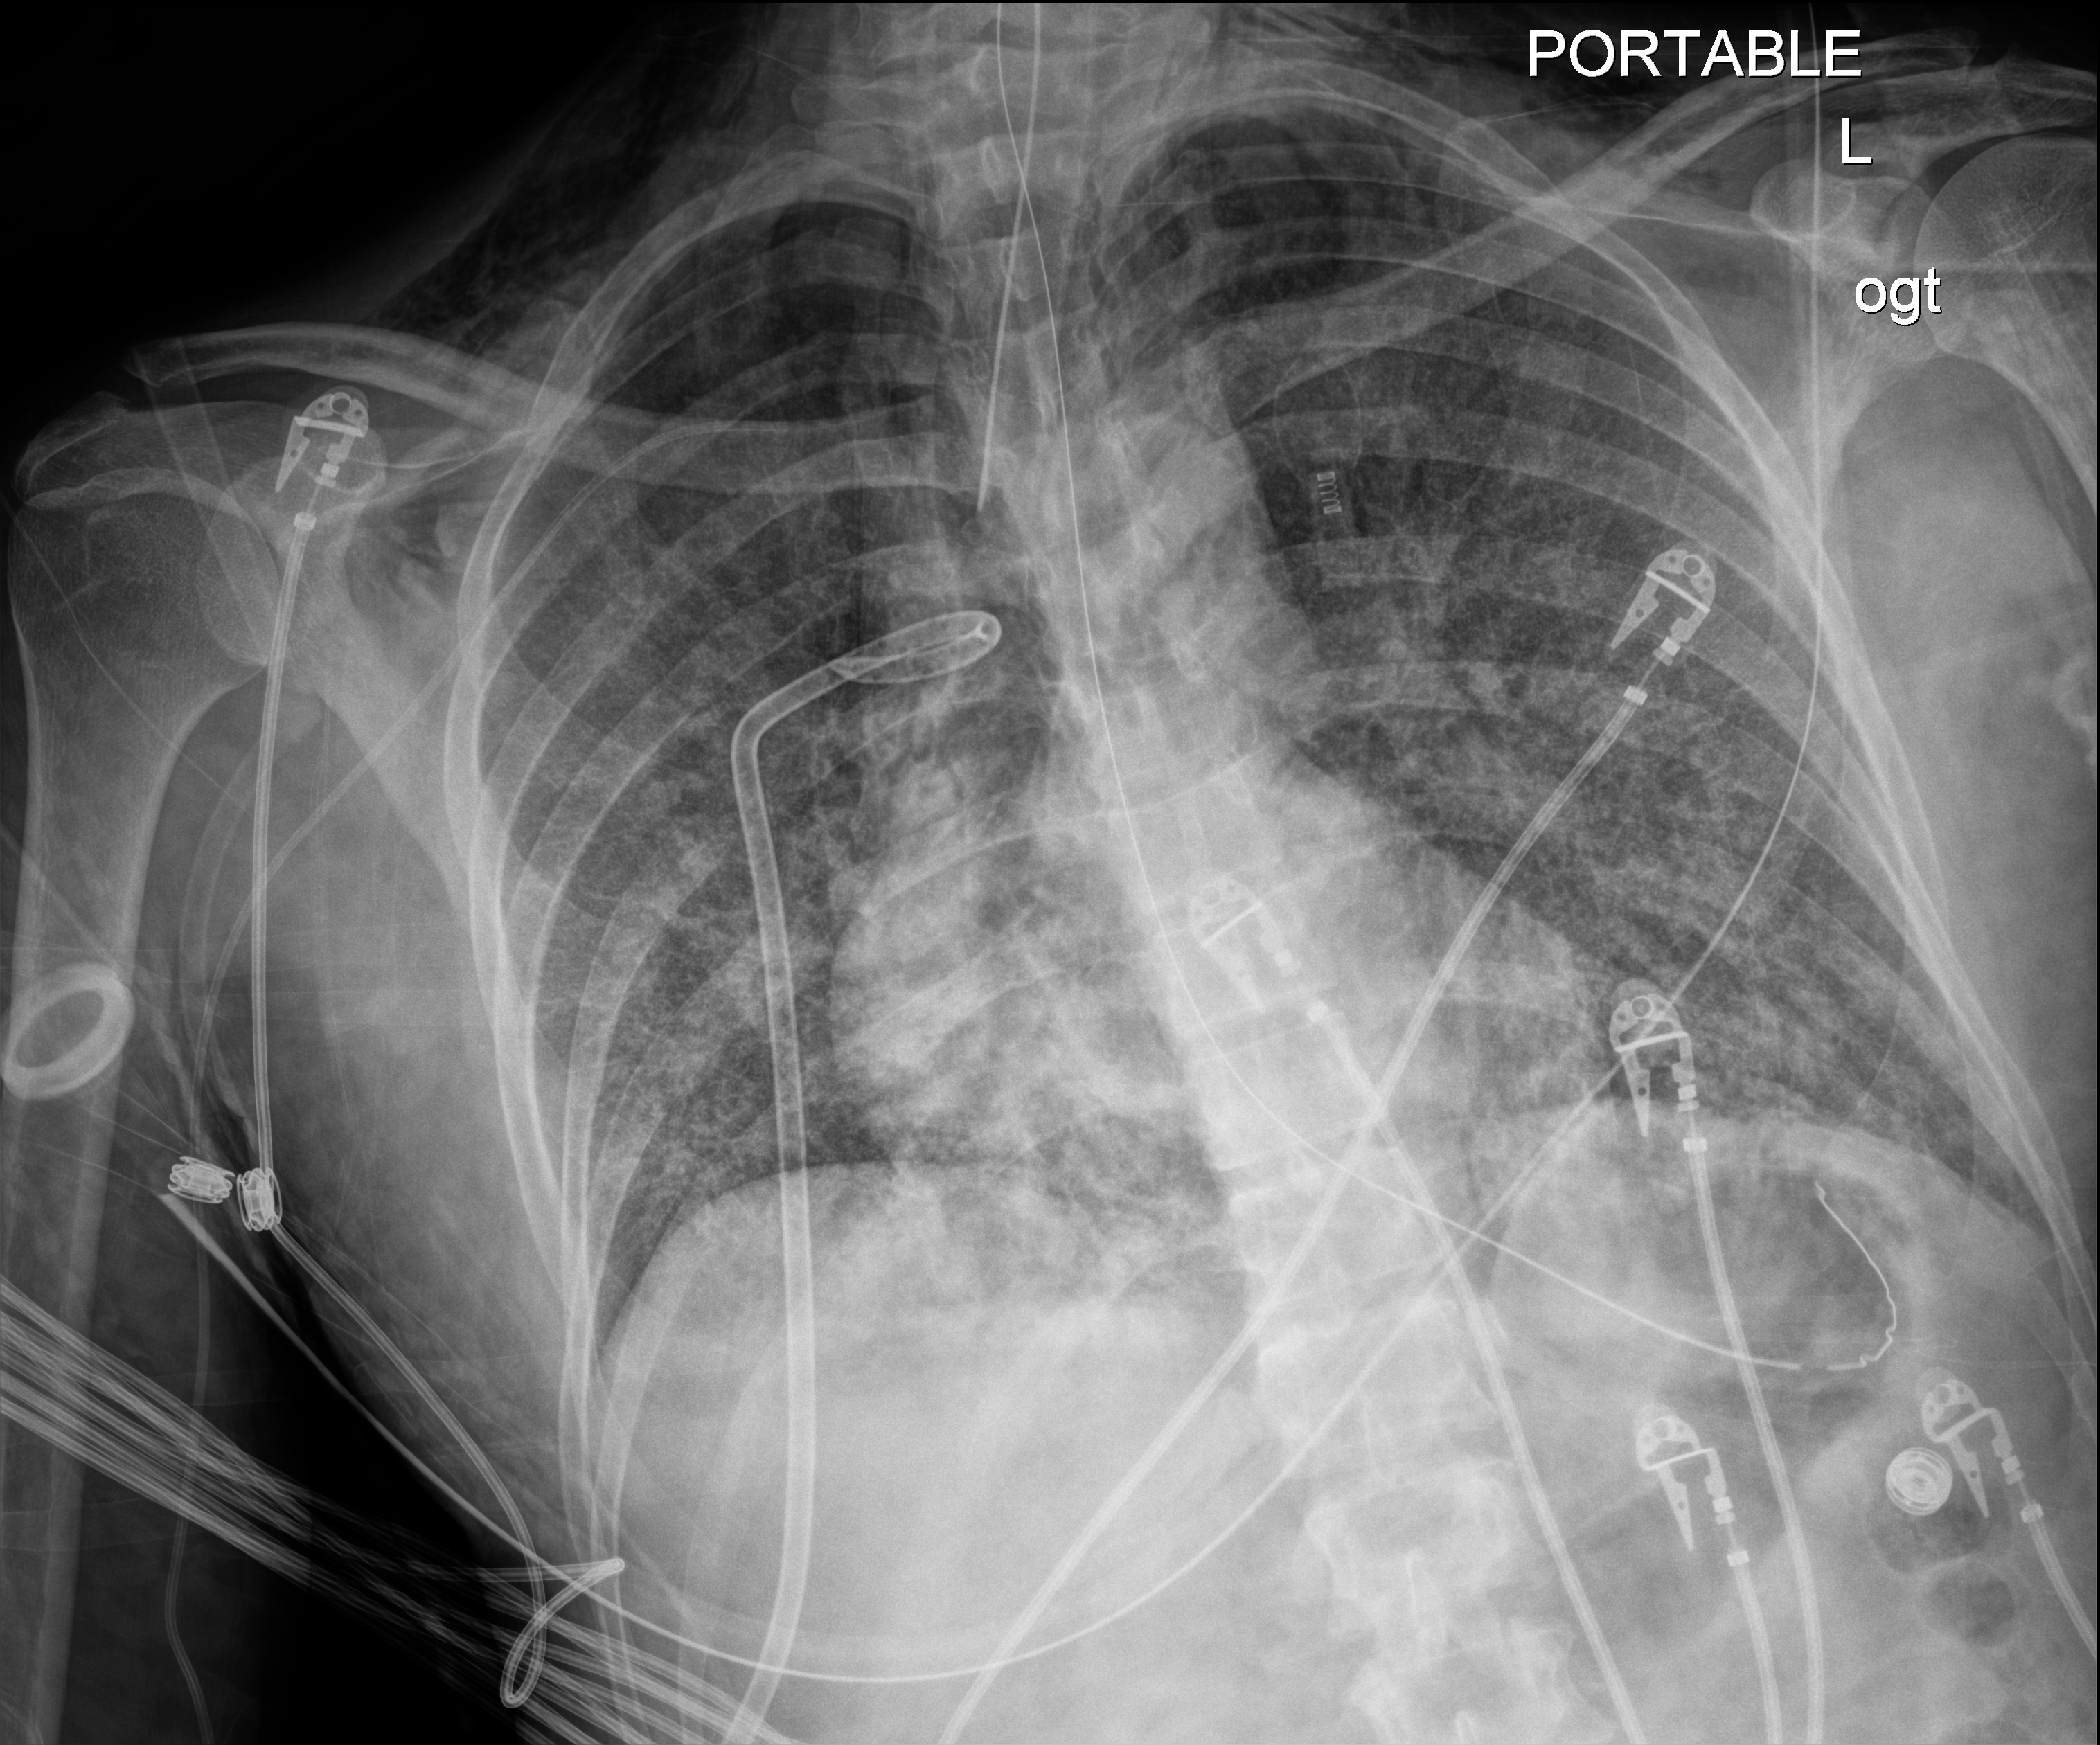
Chest radiograph (digital radiography); anteroposterior (AP) projection. Adult patient hospitalised with COVID-19, age 18–59 years.
Hospital-stay facts (about this admission, not read from this image; timing relative to this image not recorded): admitted to intensive care during this hospital stay: yes.